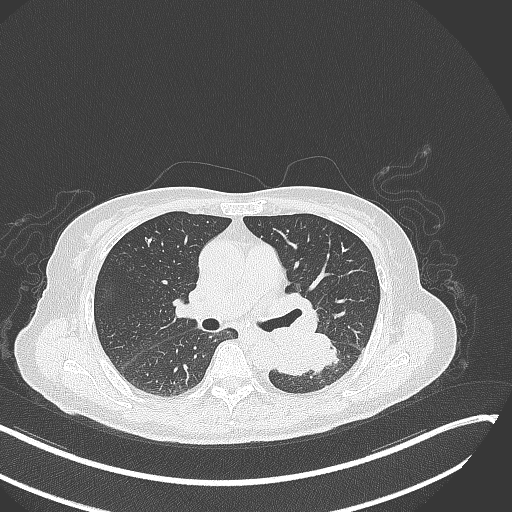
Chest CT, one axial slice. Position 162 of 342 along the scan axis. Reconstruction kernel B70f. 120 kVp. Lung window (W 1500 / L -600 HU). 512 × 512 image matrix, field of view 400 × 400 mm. Patient: female, 64 years. Case-level facts recorded for this patient, not image findings: clinical TNM (as recorded): T3 N1 M1.
Structures marked on this image (bounding box drawn by a radiologist):
- lung tumour (recorded histology: small cell carcinoma): bounding box <271,326,345,376> (left, top, right, bottom; pixels)